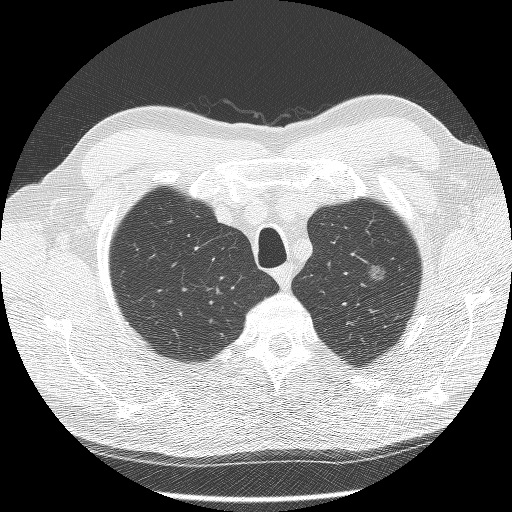
Chest CT (low-dose screening protocol), one axial image; second annual screen; lung window (W 1500 / L -600 HU); 2.5 mm slice thickness; lung (sharp) reconstruction kernel (BONE); 512 × 512 image matrix, field of view 350 × 350 mm. Male participant, aged 60 years at enrolment. Former smoker at enrolment.
Expert-annotated lung lesion, bounding box [x1, y1, x2, y2] px = [349, 255, 401, 298]. The screening reader recorded 2 non-calcified nodules or masses ≥4 mm on this exam (right lower lobe, left upper lobe); which of them this box marks is not recorded. Lung cancer was diagnosed 448 days after this screen: bronchiolo-alveolar carcinoma, non-mucinous, left upper lobe, well differentiated (G1), stage IA (AJCC 6th edition), 16 mm at pathology.